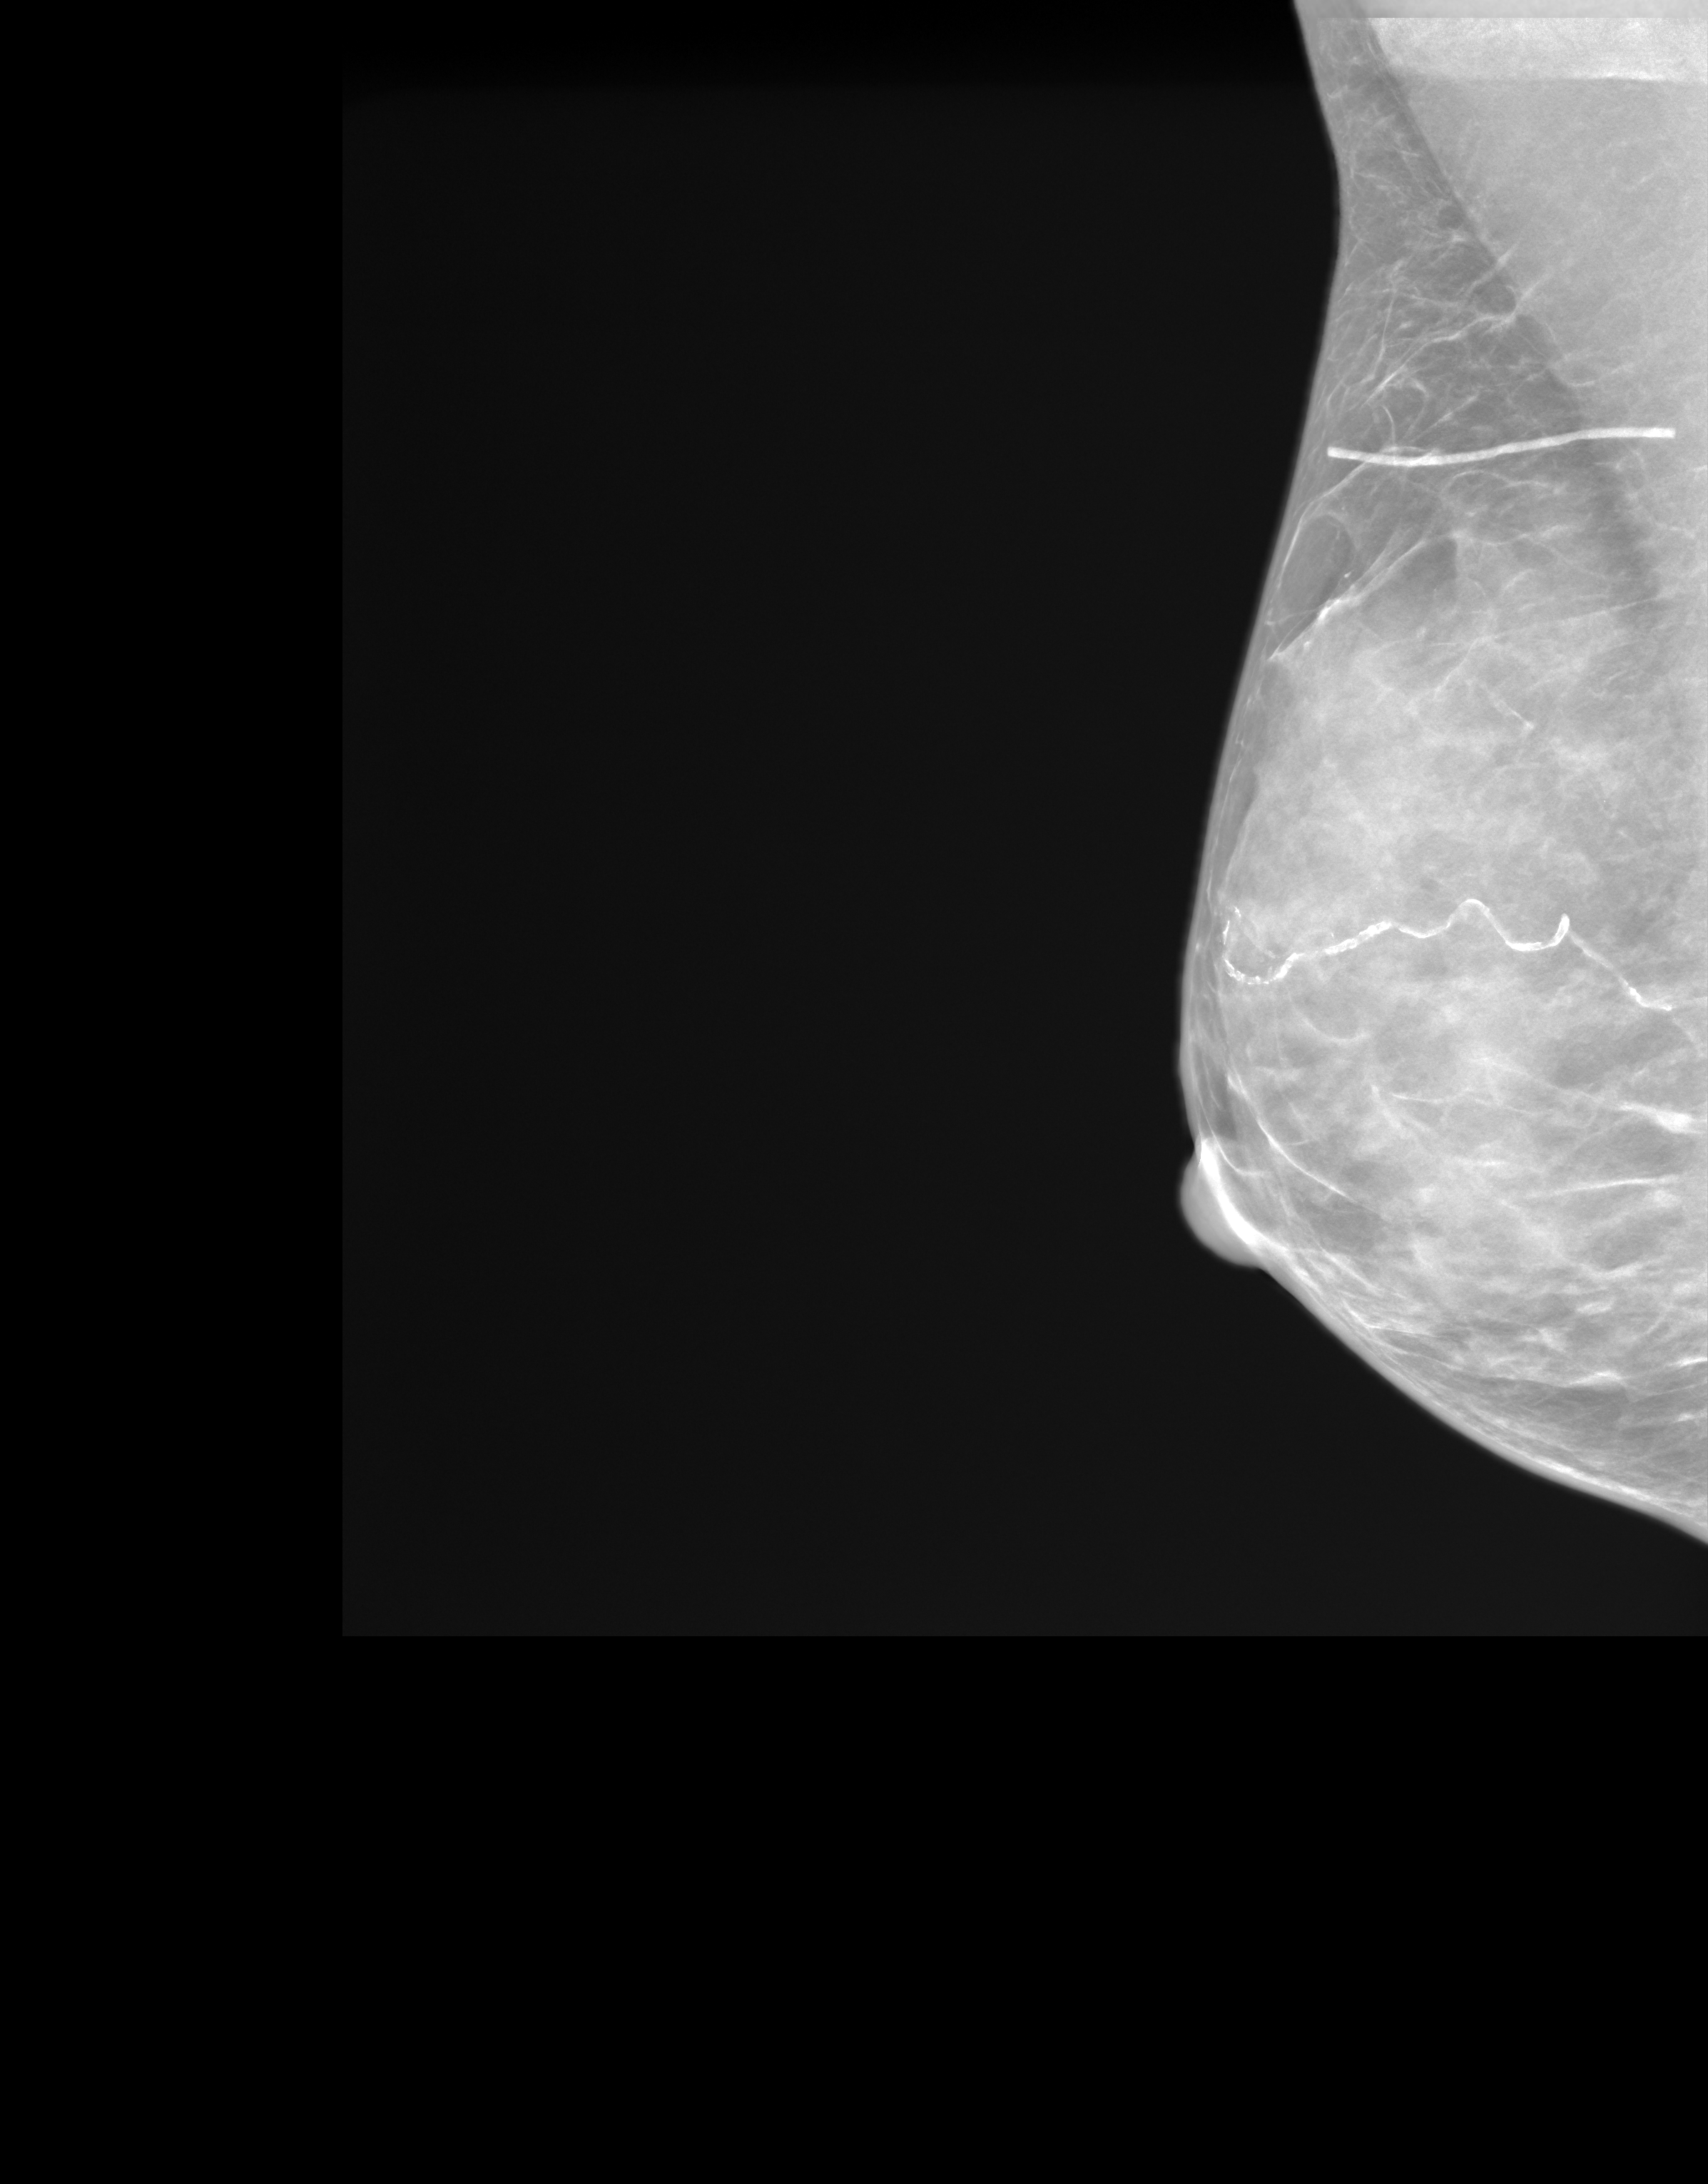
Screening examination. Female patient, age 60 years.
Image type: synthesized 2-D view from tomosynthesis. Breast: right. Projection: mediolateral oblique (MLO) view.